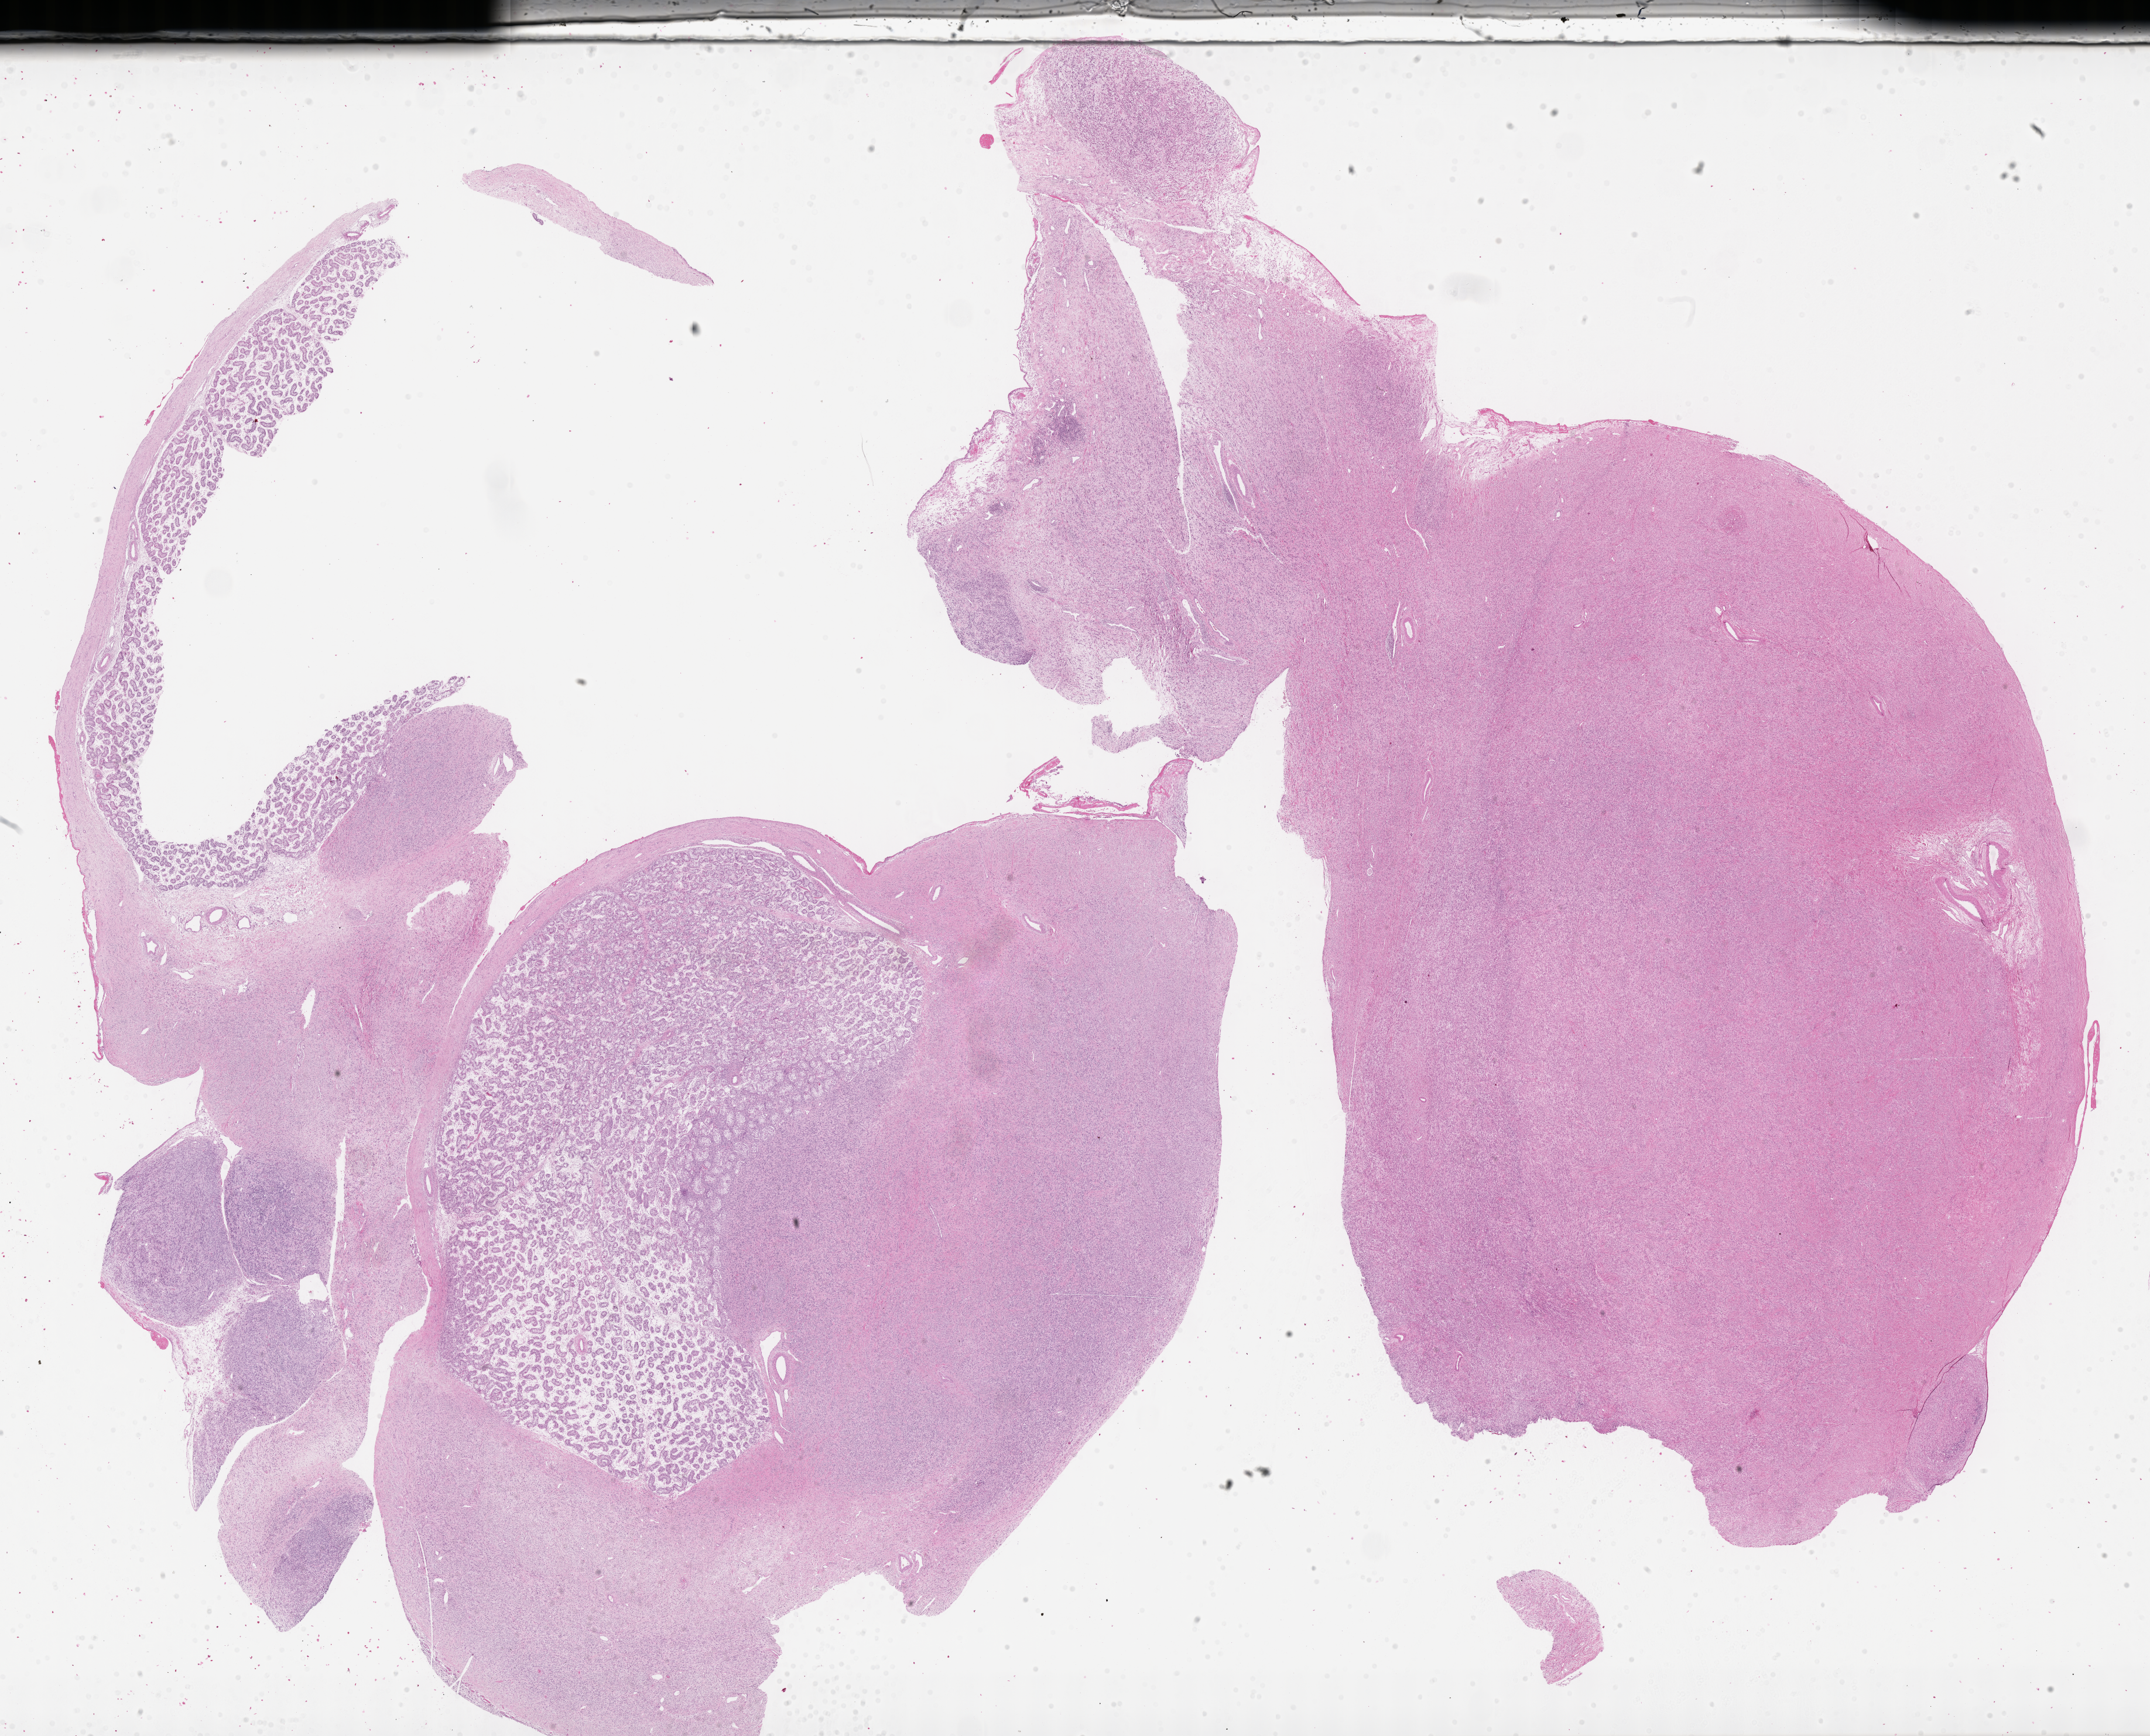
Whole-slide image, hematoxylin and eosin (H&E) stain of tumor tissue, low-resolution overview of the scanned area, about 29.7 x 24.0 mm, formalin-fixed, paraffin-embedded (FFPE) tissue, sample anatomic site: testicle-right. Male patient, age at diagnosis 8.6 years.
Metastatic status at presentation (as recorded): non-metastatic. Diagnosis: rhabdomyosarcoma; histological classification: embryonal rhabdomyosarcoma. Stage (as recorded): 1.